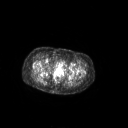
FDG PET of an extremity soft-tissue mass (from a PET/CT study), one axial slice. Slice 62 of 267 in the series (ordered by position). 3.27 mm slice thickness. 128 × 128 image matrix. Female patient, age 70 years. From the clinical record (not read from this slice): histological type: synovial sarcoma; grade: intermediate; site of the primary tumour: right buttock.
Structures marked on this image (expert contour drawn on MRI and transferred to this co-registered scan by the dataset authors):
- gross tumour volume including surrounding oedema: bounding box [x1, y1, x2, y2] px = [34, 70, 45, 79]